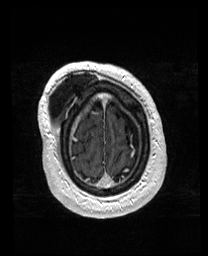
Brain MRI from a brain-tumour surgery series, one axial slice. Position 33 of 176 along the scan axis. T1-weighted post-contrast. 1 mm slice thickness. 208 × 256 image matrix. From the clinical record (not read from this slice): histopathology: Astrocytoma; WHO grade: 4; IDH mutation: yes.
Outlined on this slice (manually delineated by an expert):
- previous resection cavity: bounding box <56,95,106,111> (left, top, right, bottom; pixels)